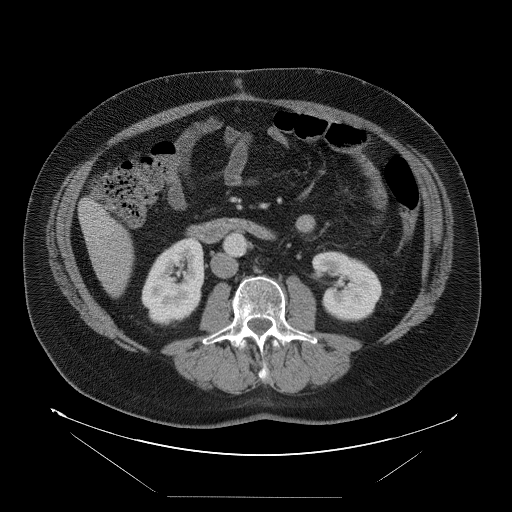
Contrast-enhanced abdominal CT, one axial slice. Slice 22 of 114 in the series (ordered by position). 120 kVp. Intravenous contrast given. Soft-tissue window (W 400 / L 40 HU). 512 × 512 image matrix, field of view 500 × 500 mm. Male patient, age 61 years. From the clinical record (not read from this slice): diagnosis: colorectal cancer liver metastases, imaged before liver resection.
Annotated regions visible in this slice (expert manual segmentation):
- liver: box from (x=81, y=200) to (x=133, y=296) px